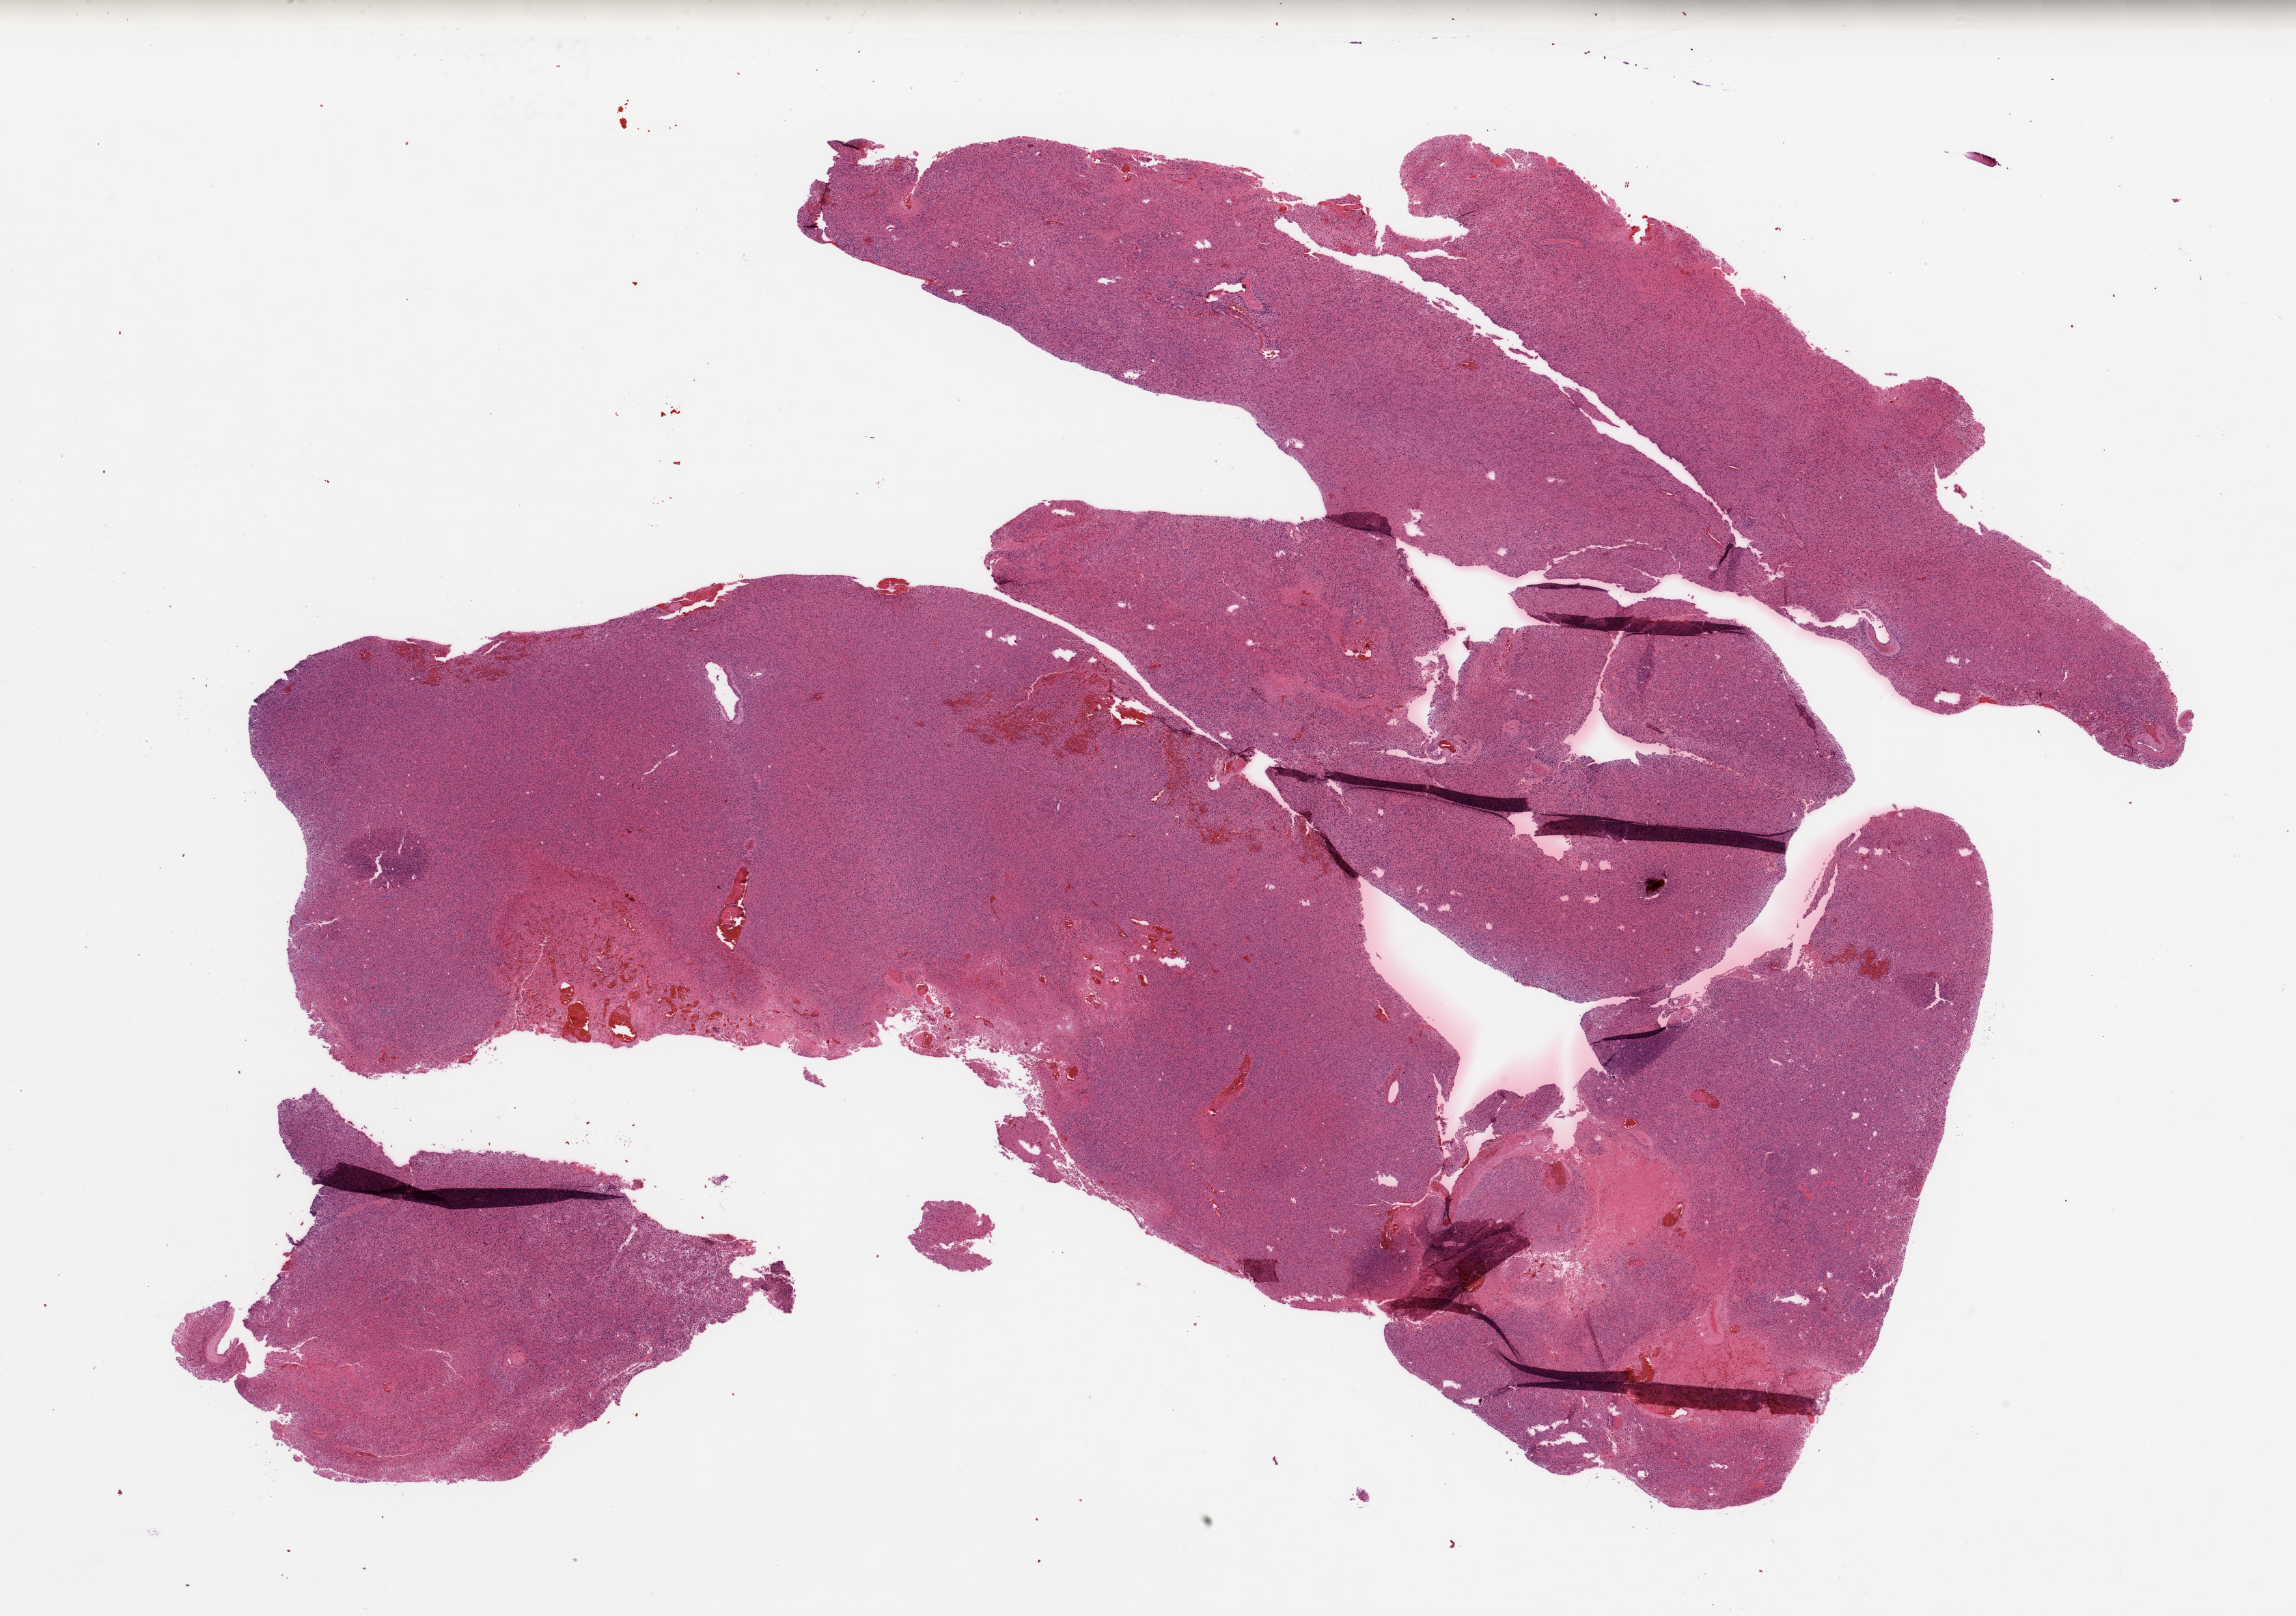
Hematoxylin and eosin (H&E) stained whole-slide image, a low-resolution overview of the entire scanned area, about 26.6 x 18.7 mm. Brain, tumour tissue. Patient: female, age 63 years.
* histologic diagnosis: Glioblastoma
* primary tumour site (as recorded): parietal lobe